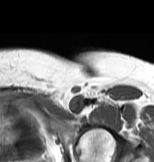
MRI of an extremity soft-tissue mass, one axial slice; slice 63 of 83 in the series (ordered by position); MR volume resampled by the dataset authors to the PET/CT grid (not the native acquisition matrix); 3.27 mm slice thickness; 154 × 162 image matrix, field of view 150 × 158 mm. Female patient. Case-level facts recorded for this patient, not image findings: histological type: myxofibrosarcoma; grade: intermediate; site of the primary tumour: left thigh.
Annotated regions visible in this slice (expert contour drawn on MRI and transferred to this co-registered scan by the dataset authors):
- gross tumour volume including surrounding oedema: bounding box [x1, y1, x2, y2] px = [71, 98, 86, 115]